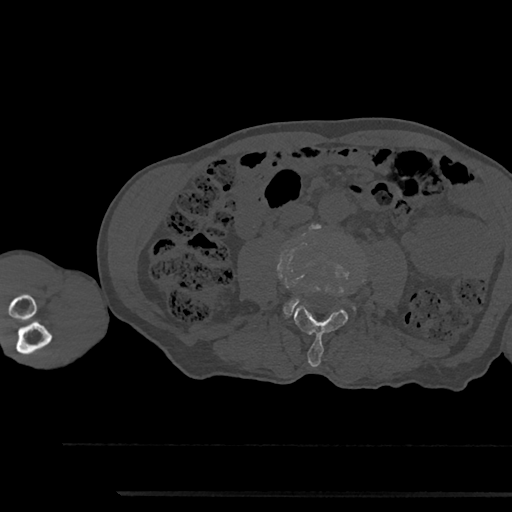
CT including the spine, one axial slice. Position 457 of 797 along the scan axis. Reconstruction kernel Br40s/3. 120 kVp. Bone window (W 1800 / L 400 HU). 512 × 512 image matrix, field of view 367 × 367 mm. Male patient, age 79 years. From the clinical record (not read from this slice): primary cancer: prostate.
Annotated regions visible in this slice (semi-automatically segmented with operator editing):
- L3 vertebra: bounding box <294,306,348,367> (left, top, right, bottom; pixels)
- L4 vertebra: <284,299,299,316>